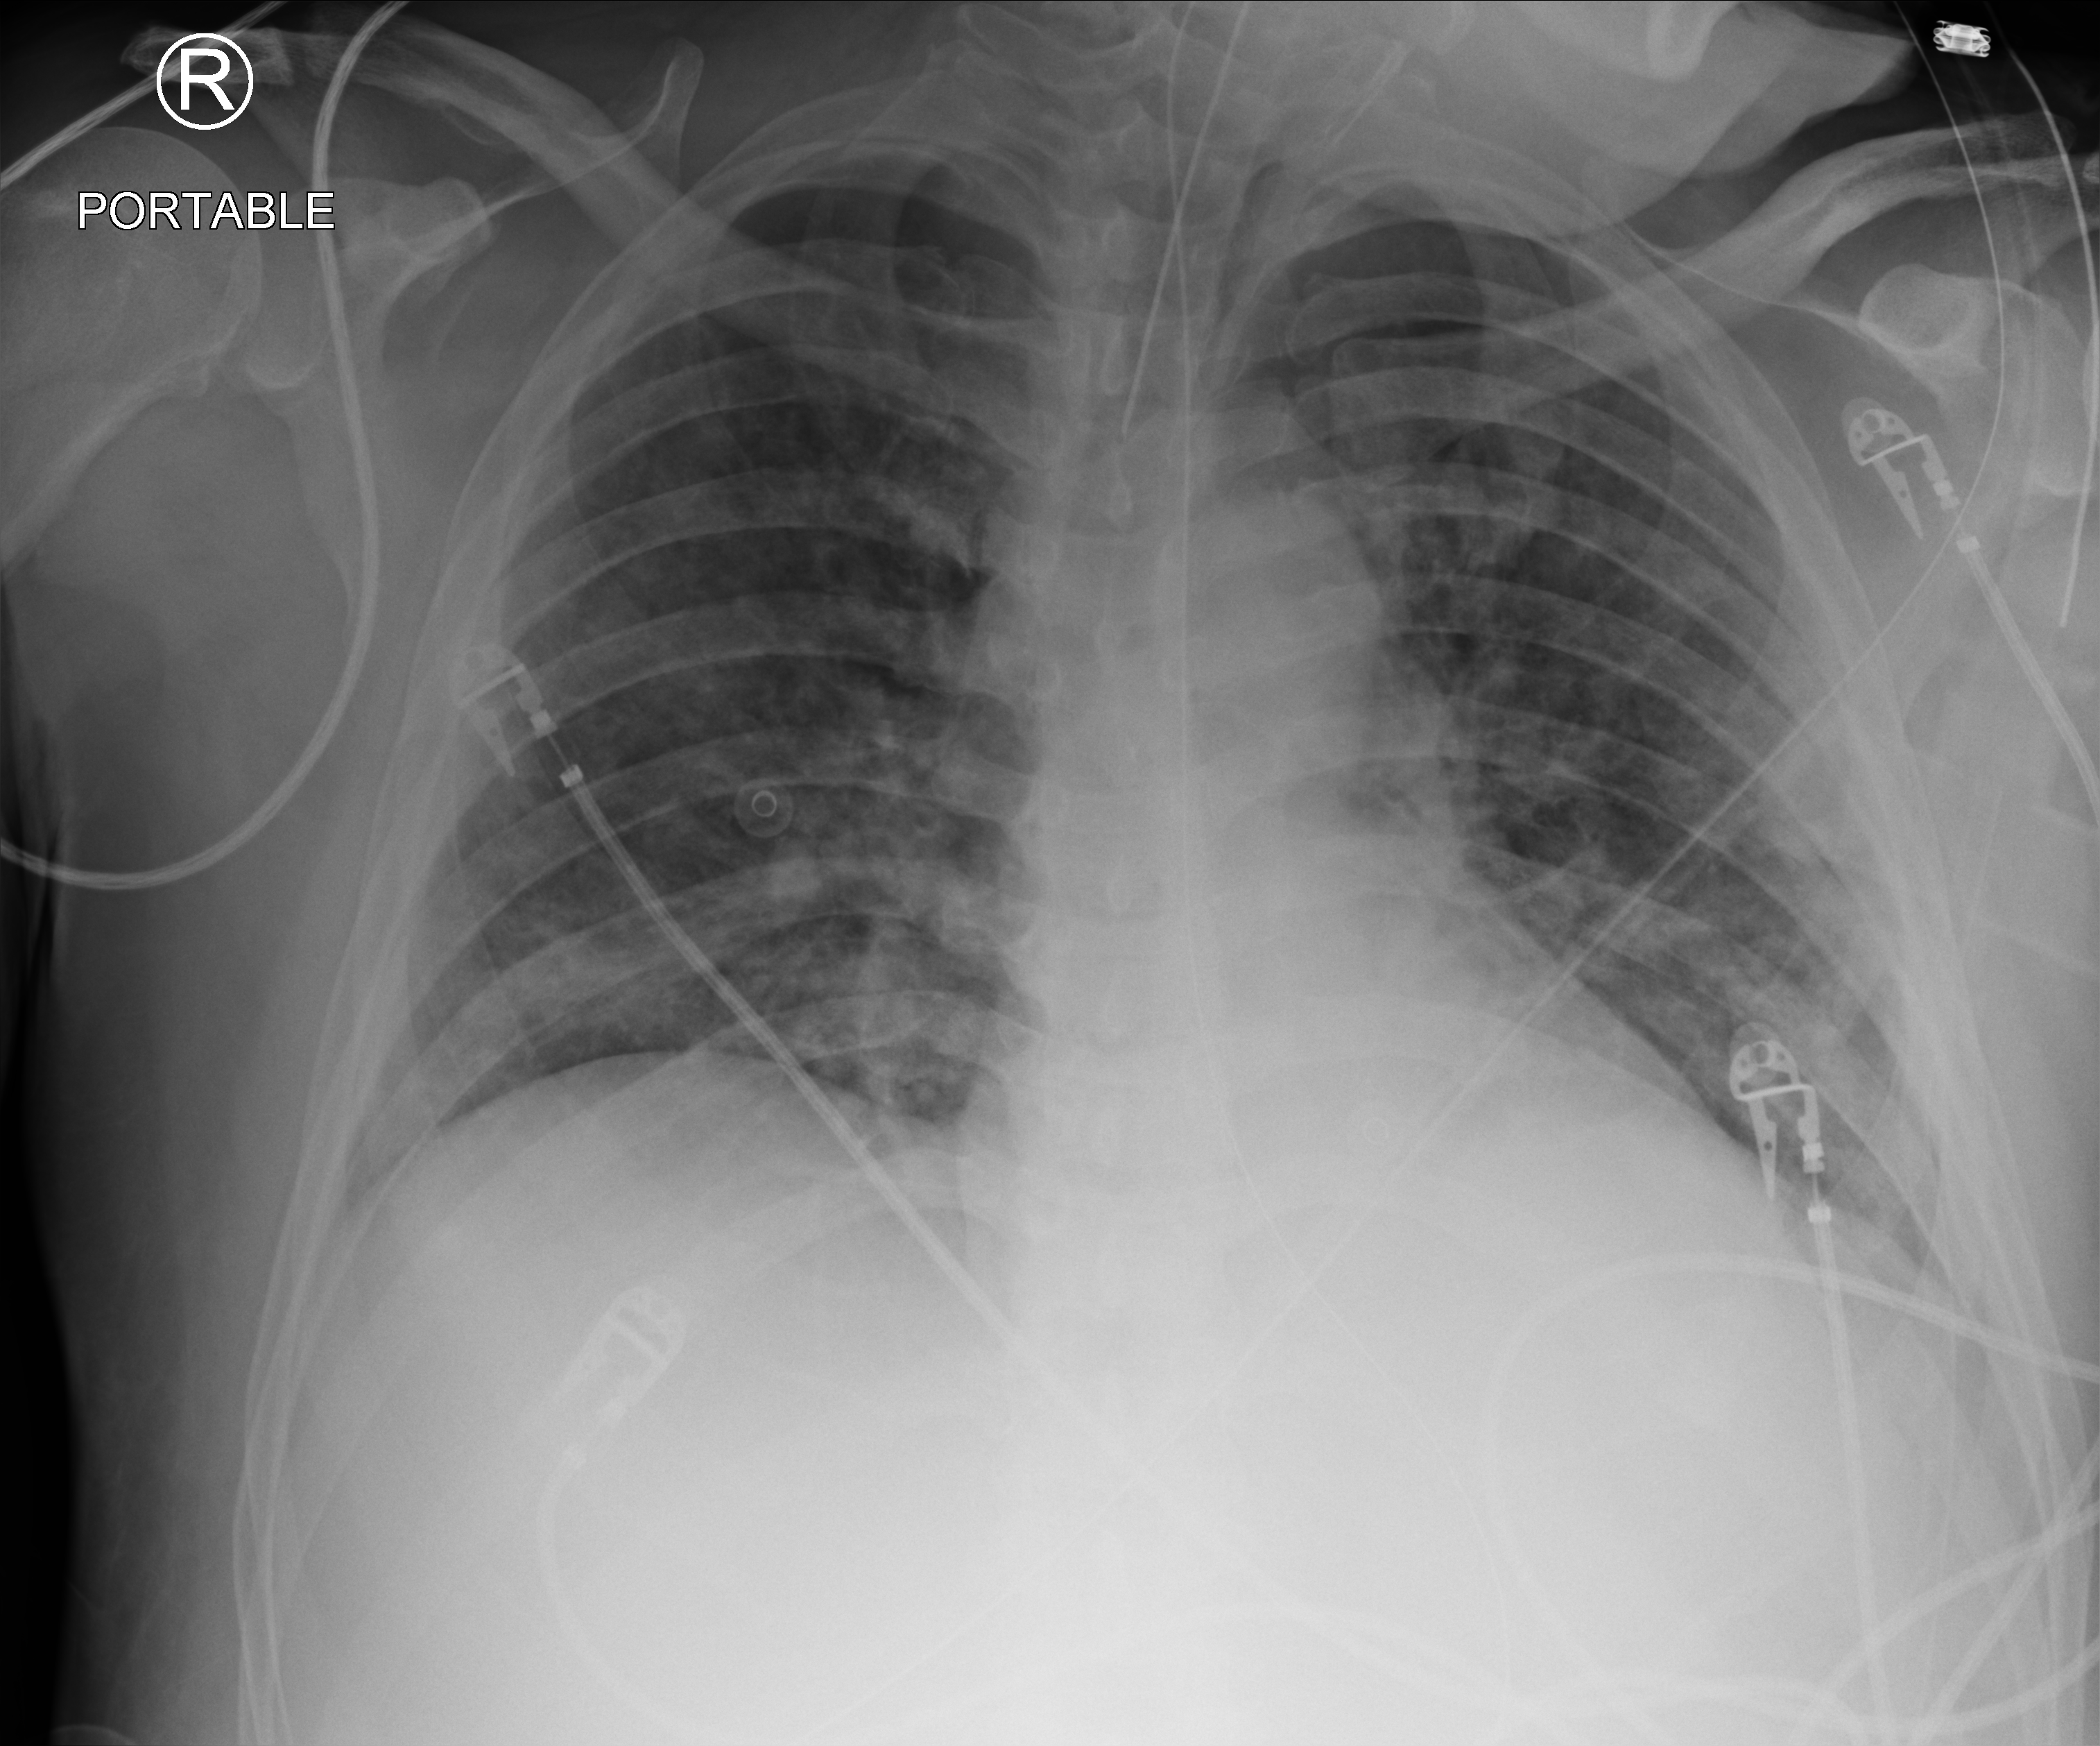
Bedside chest radiograph (computed radiography), anteroposterior (AP) projection. Patient hospitalised with COVID-19; male, aged 18–59 years.
Admission-level facts for this patient (not findings on this image; timing relative to this image not recorded): COPD (admission record): no; mechanically ventilated during this hospital stay: yes.